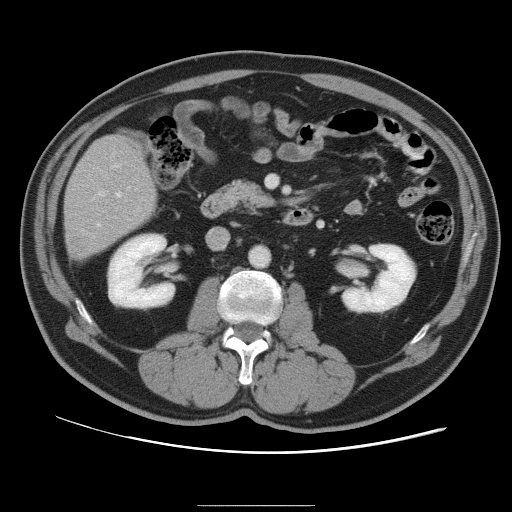
Contrast-enhanced abdominal CT, one axial slice. Position 36 of 105 along the scan axis. 120 kVp. Intravenous contrast given. Soft-tissue window (W 400 / L 40 HU). 5 mm slice thickness. 512 × 512 image matrix, field of view 399 × 399 mm. Male patient, age 64 years. From the clinical record (not read from this slice): diagnosis: colorectal cancer liver metastases, imaged before liver resection; multiple liver metastases: yes; largest metastasis: 3 cm.
Outlined on this slice (manually delineated by an expert):
- hepatic veins: box from (x=97, y=192) to (x=121, y=227) px
- liver: (x=64, y=137)–(x=156, y=258)
- planned liver remnant (the part of the liver to remain after resection): (x=65, y=137)–(x=156, y=238)
- portal vein (with intrahepatic branches): (x=98, y=165)–(x=119, y=196)
- liver metastasis: (x=71, y=239)–(x=86, y=257)